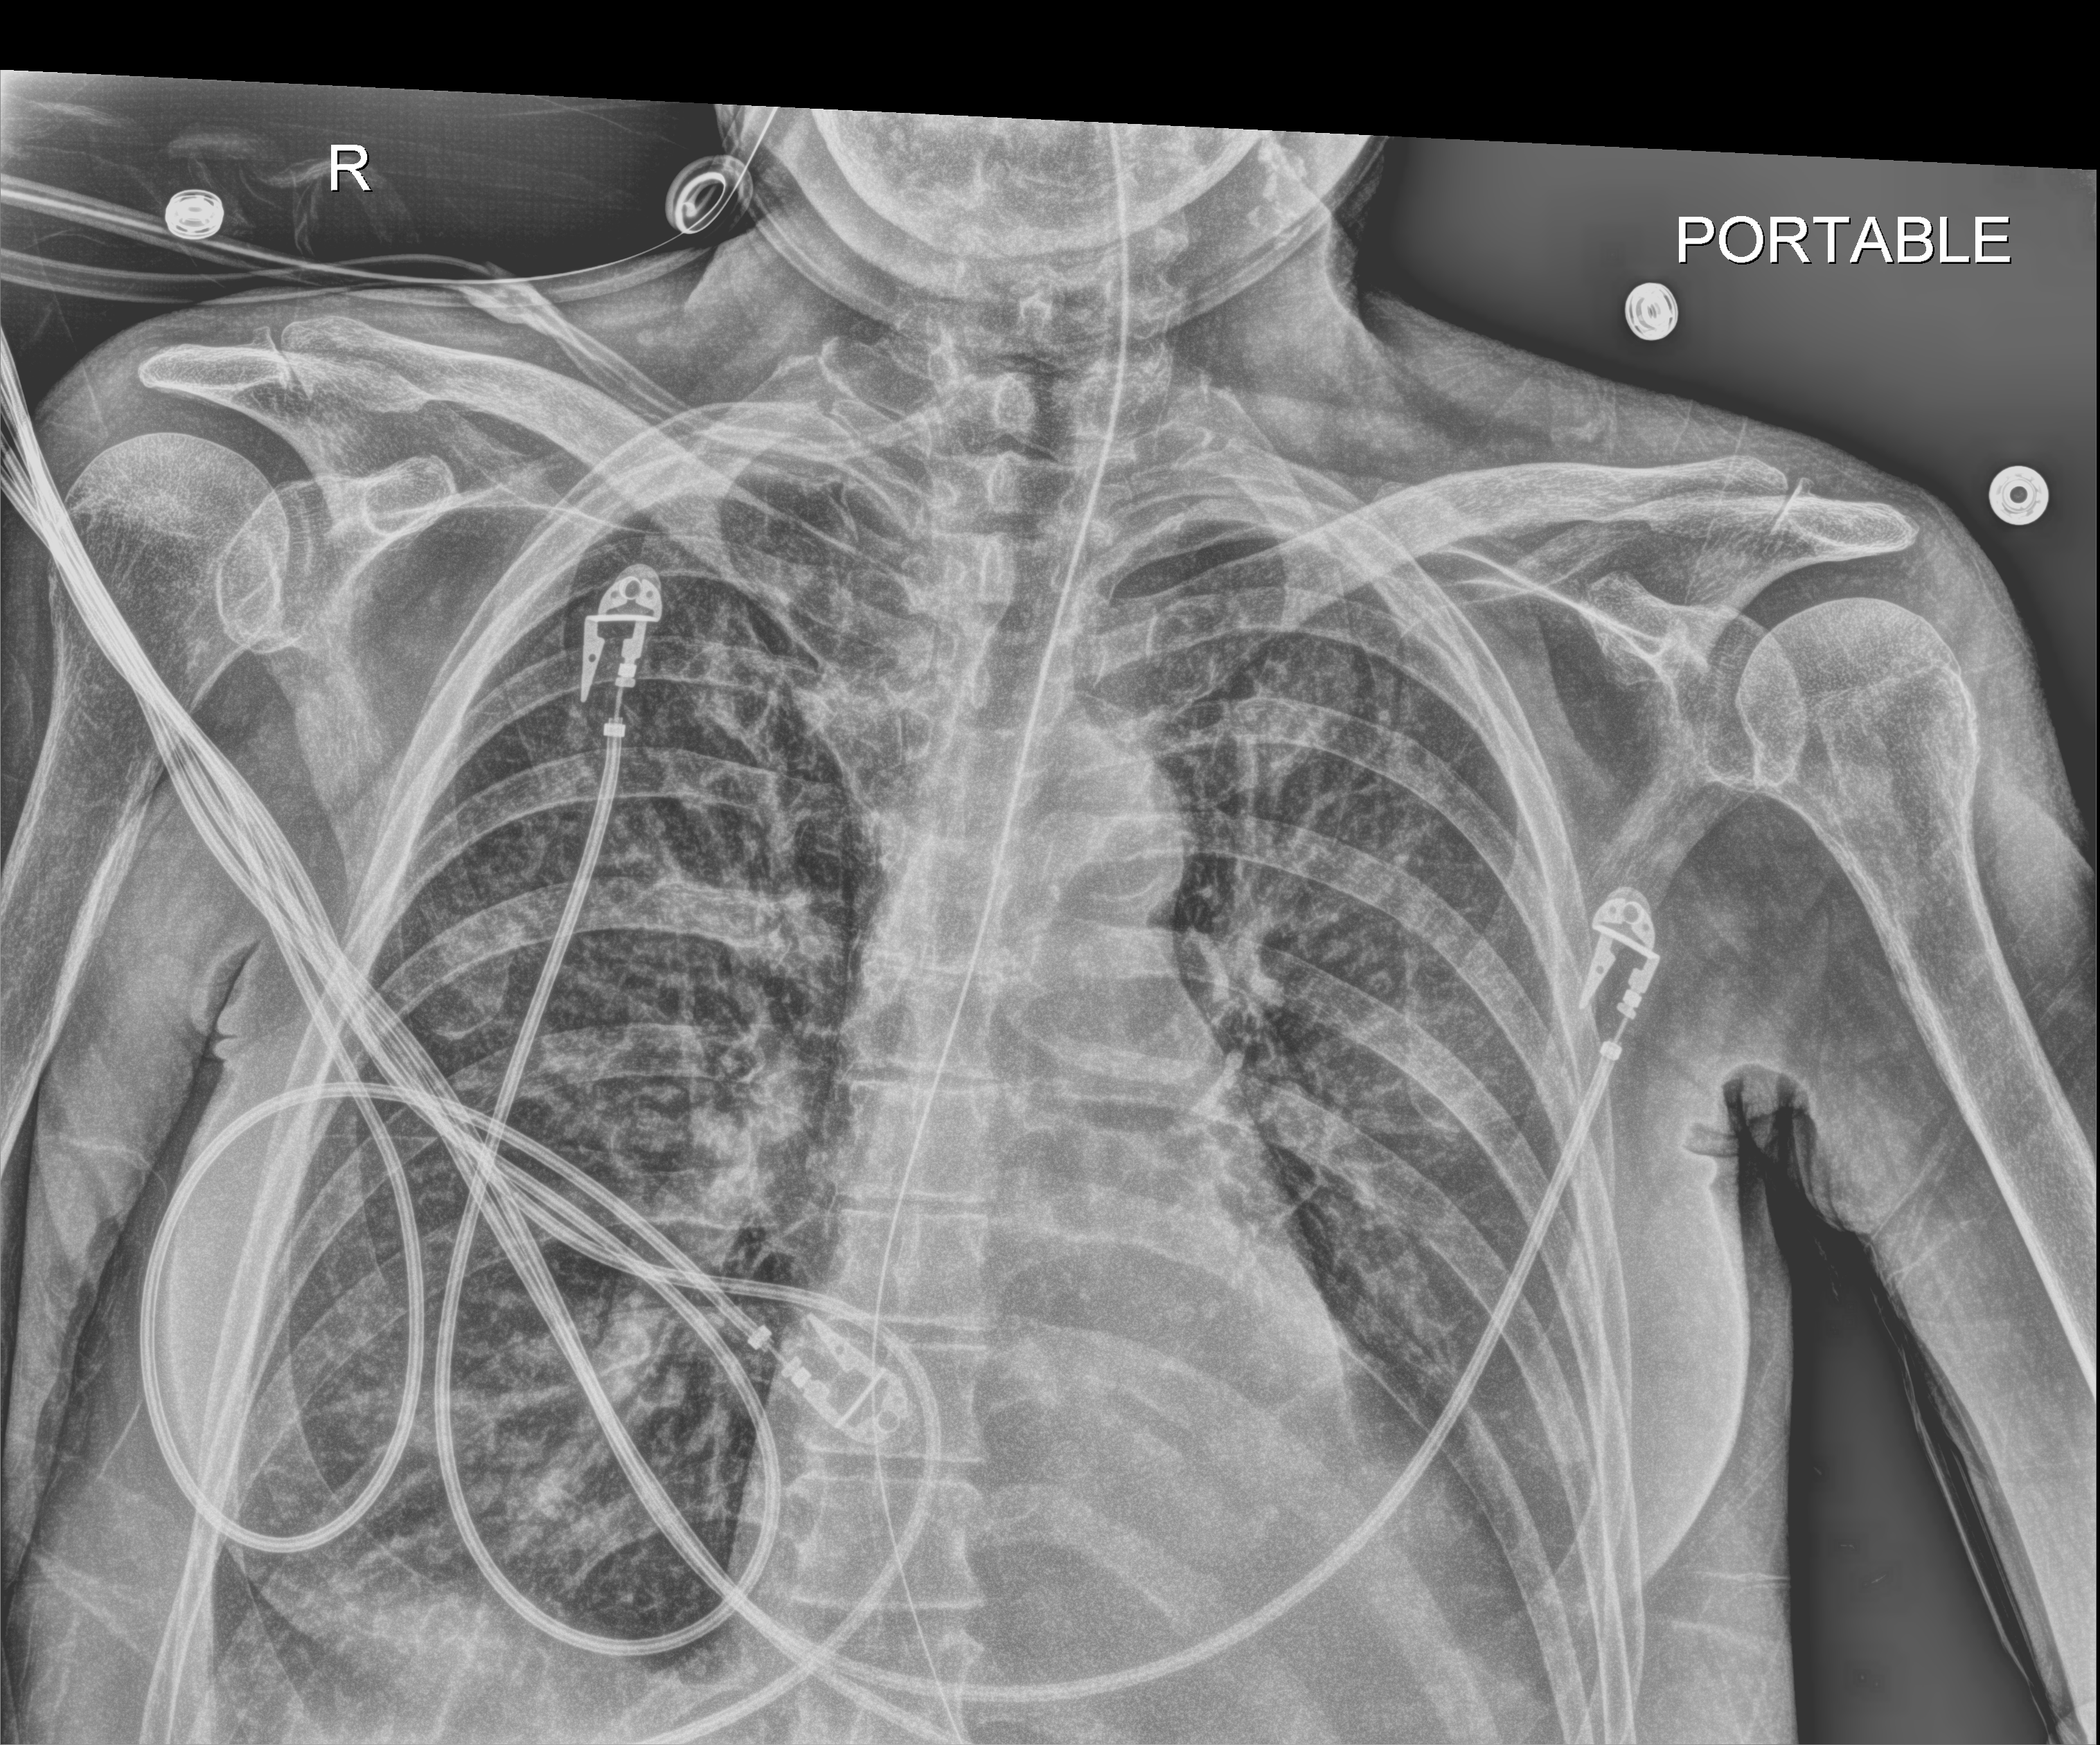
Chest X-ray (portable), anteroposterior (AP) projection. Patient hospitalised with COVID-19; female, aged 60–74 years.
Admission-level facts for this patient (not findings on this image; timing relative to this image not recorded): admitted to intensive care during this hospital stay: yes.